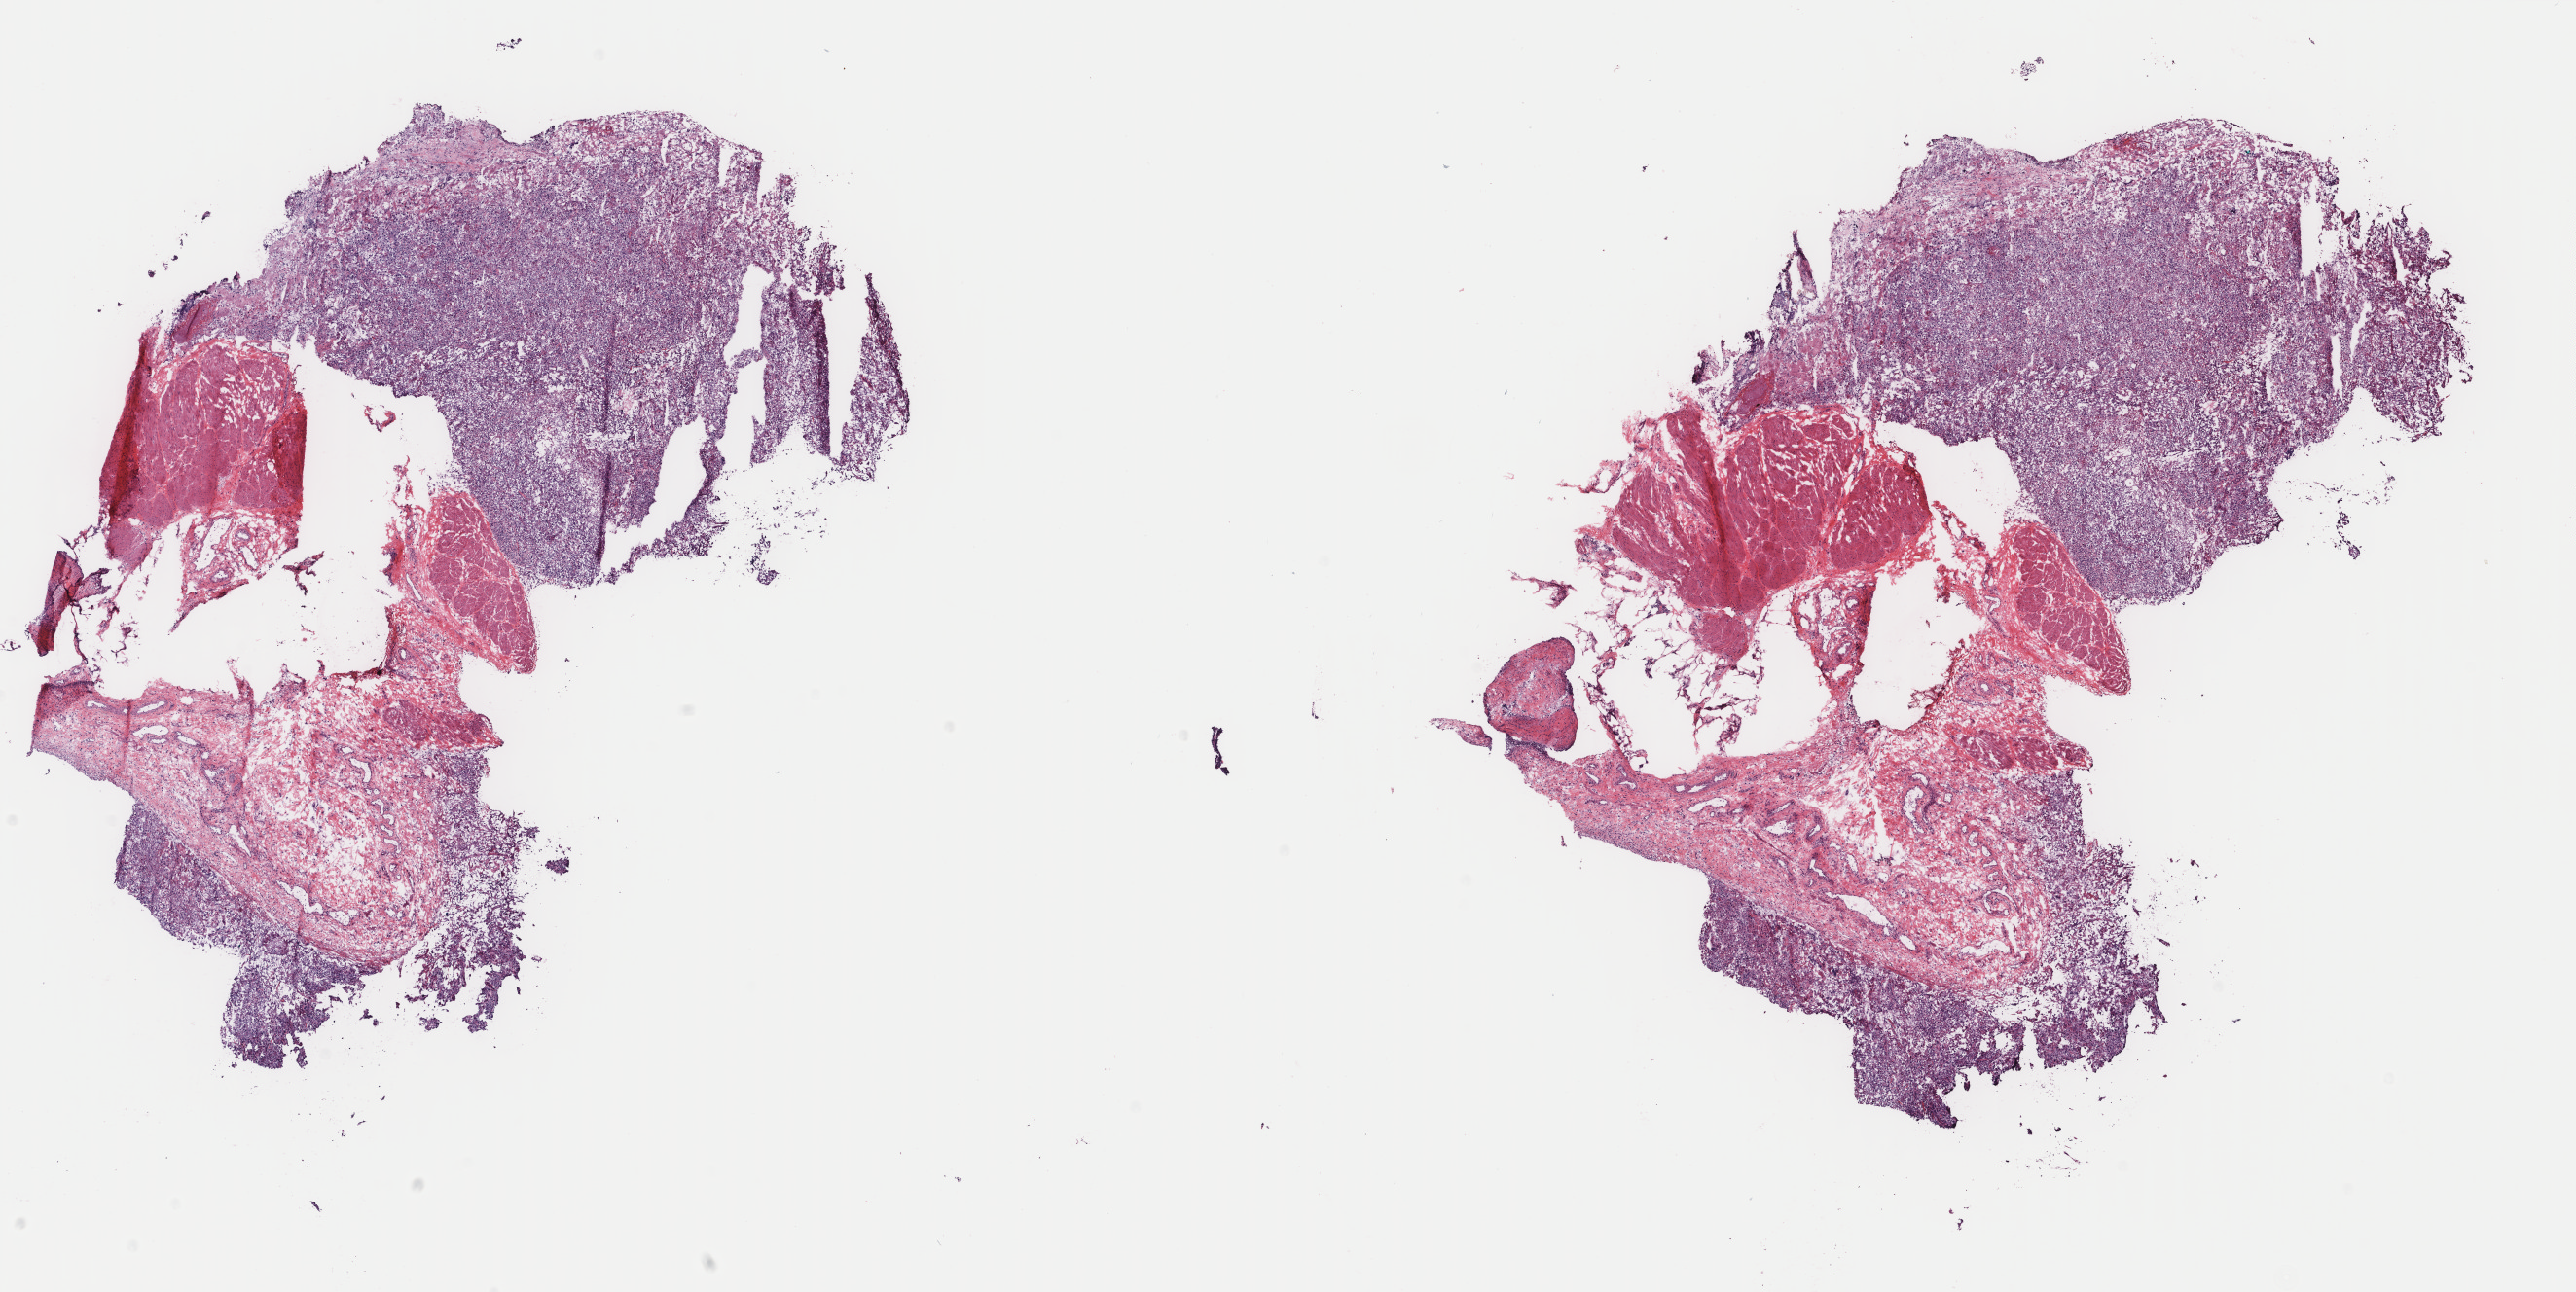
Digitized Hematoxylin and eosin (H&E) stained tissue section (whole slide), low-resolution overview of the scanned area, about 21.0 x 10.5 mm; frozen section; bladder, primary tumour sample. Male patient; age at initial diagnosis 62 years. Histologic grade: high grade. Composition of this section per pathologist review: tumour cells 50%, tumour nuclei 65%, normal cells 0%, stromal cells 50%, necrosis 0%. Inflammatory infiltration, as recorded: lymphocyte infiltration 0%, monocyte infiltration 0%, neutrophil infiltration 0%.
Lymph nodes positive (case pathology): 0 of 19 examined. AJCC pathologic stage: II (7th edition). Pathologic diagnosis: Transitional cell carcinoma.